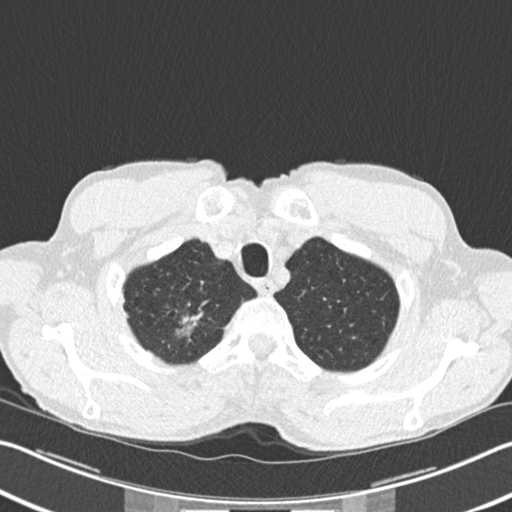
Chest CT (low-dose screening protocol), one axial image, second annual screen, lung window (W 1500 / L -600 HU), 2 mm slice thickness, standard (soft-tissue) reconstruction kernel (B30f), slice 24 of 220 in the series, 512 × 512 image matrix. Male, age 62 years at enrolment.
Expert reader's lesion annotation, bounding box (x1, y1, x2, y2) in pixels: (165, 300, 208, 345). The screening reader recorded 2 non-calcified nodules or masses ≥4 mm on this exam (right upper lobe, right upper lobe); which of them this box marks is not recorded. Official screen result: positive, change unspecified: nodule(s) >= 4 mm or enlarging nodule(s), mass(es), or other non-specific abnormalities suspicious for lung cancer. Participant outcome: lung cancer diagnosed 5 days after this screen — bronchiolo-alveolar adenocarcinoma, NOS, right upper lobe, well differentiated (G1), stage IA (AJCC 6th edition), 15 mm at pathology.